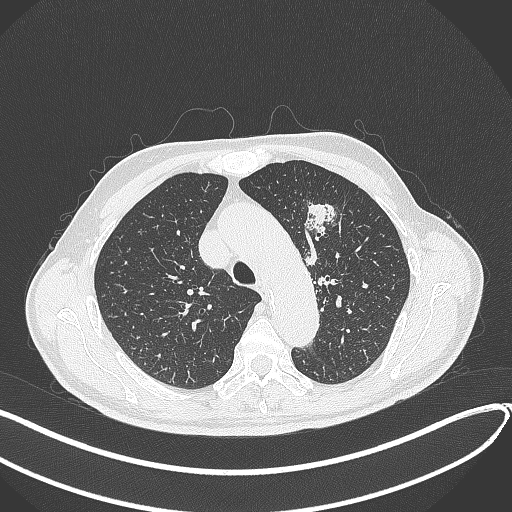
Chest CT, one axial slice; position 307 of 459 along the scan axis; reconstruction kernel B70f; 120 kVp; lung window (W 1500 / L -600 HU); 1 mm slice thickness; 512 × 512 image matrix, field of view 400 × 400 mm. Patient: male, 74 years. Case-level facts recorded for this patient, not image findings: clinical TNM (as recorded): T2b N0 M1c.
Structures marked on this image (rectangle marked by the reading radiologist):
- lung tumour (recorded histology: adenocarcinoma): bounding box <305,198,343,239> (left, top, right, bottom; pixels)